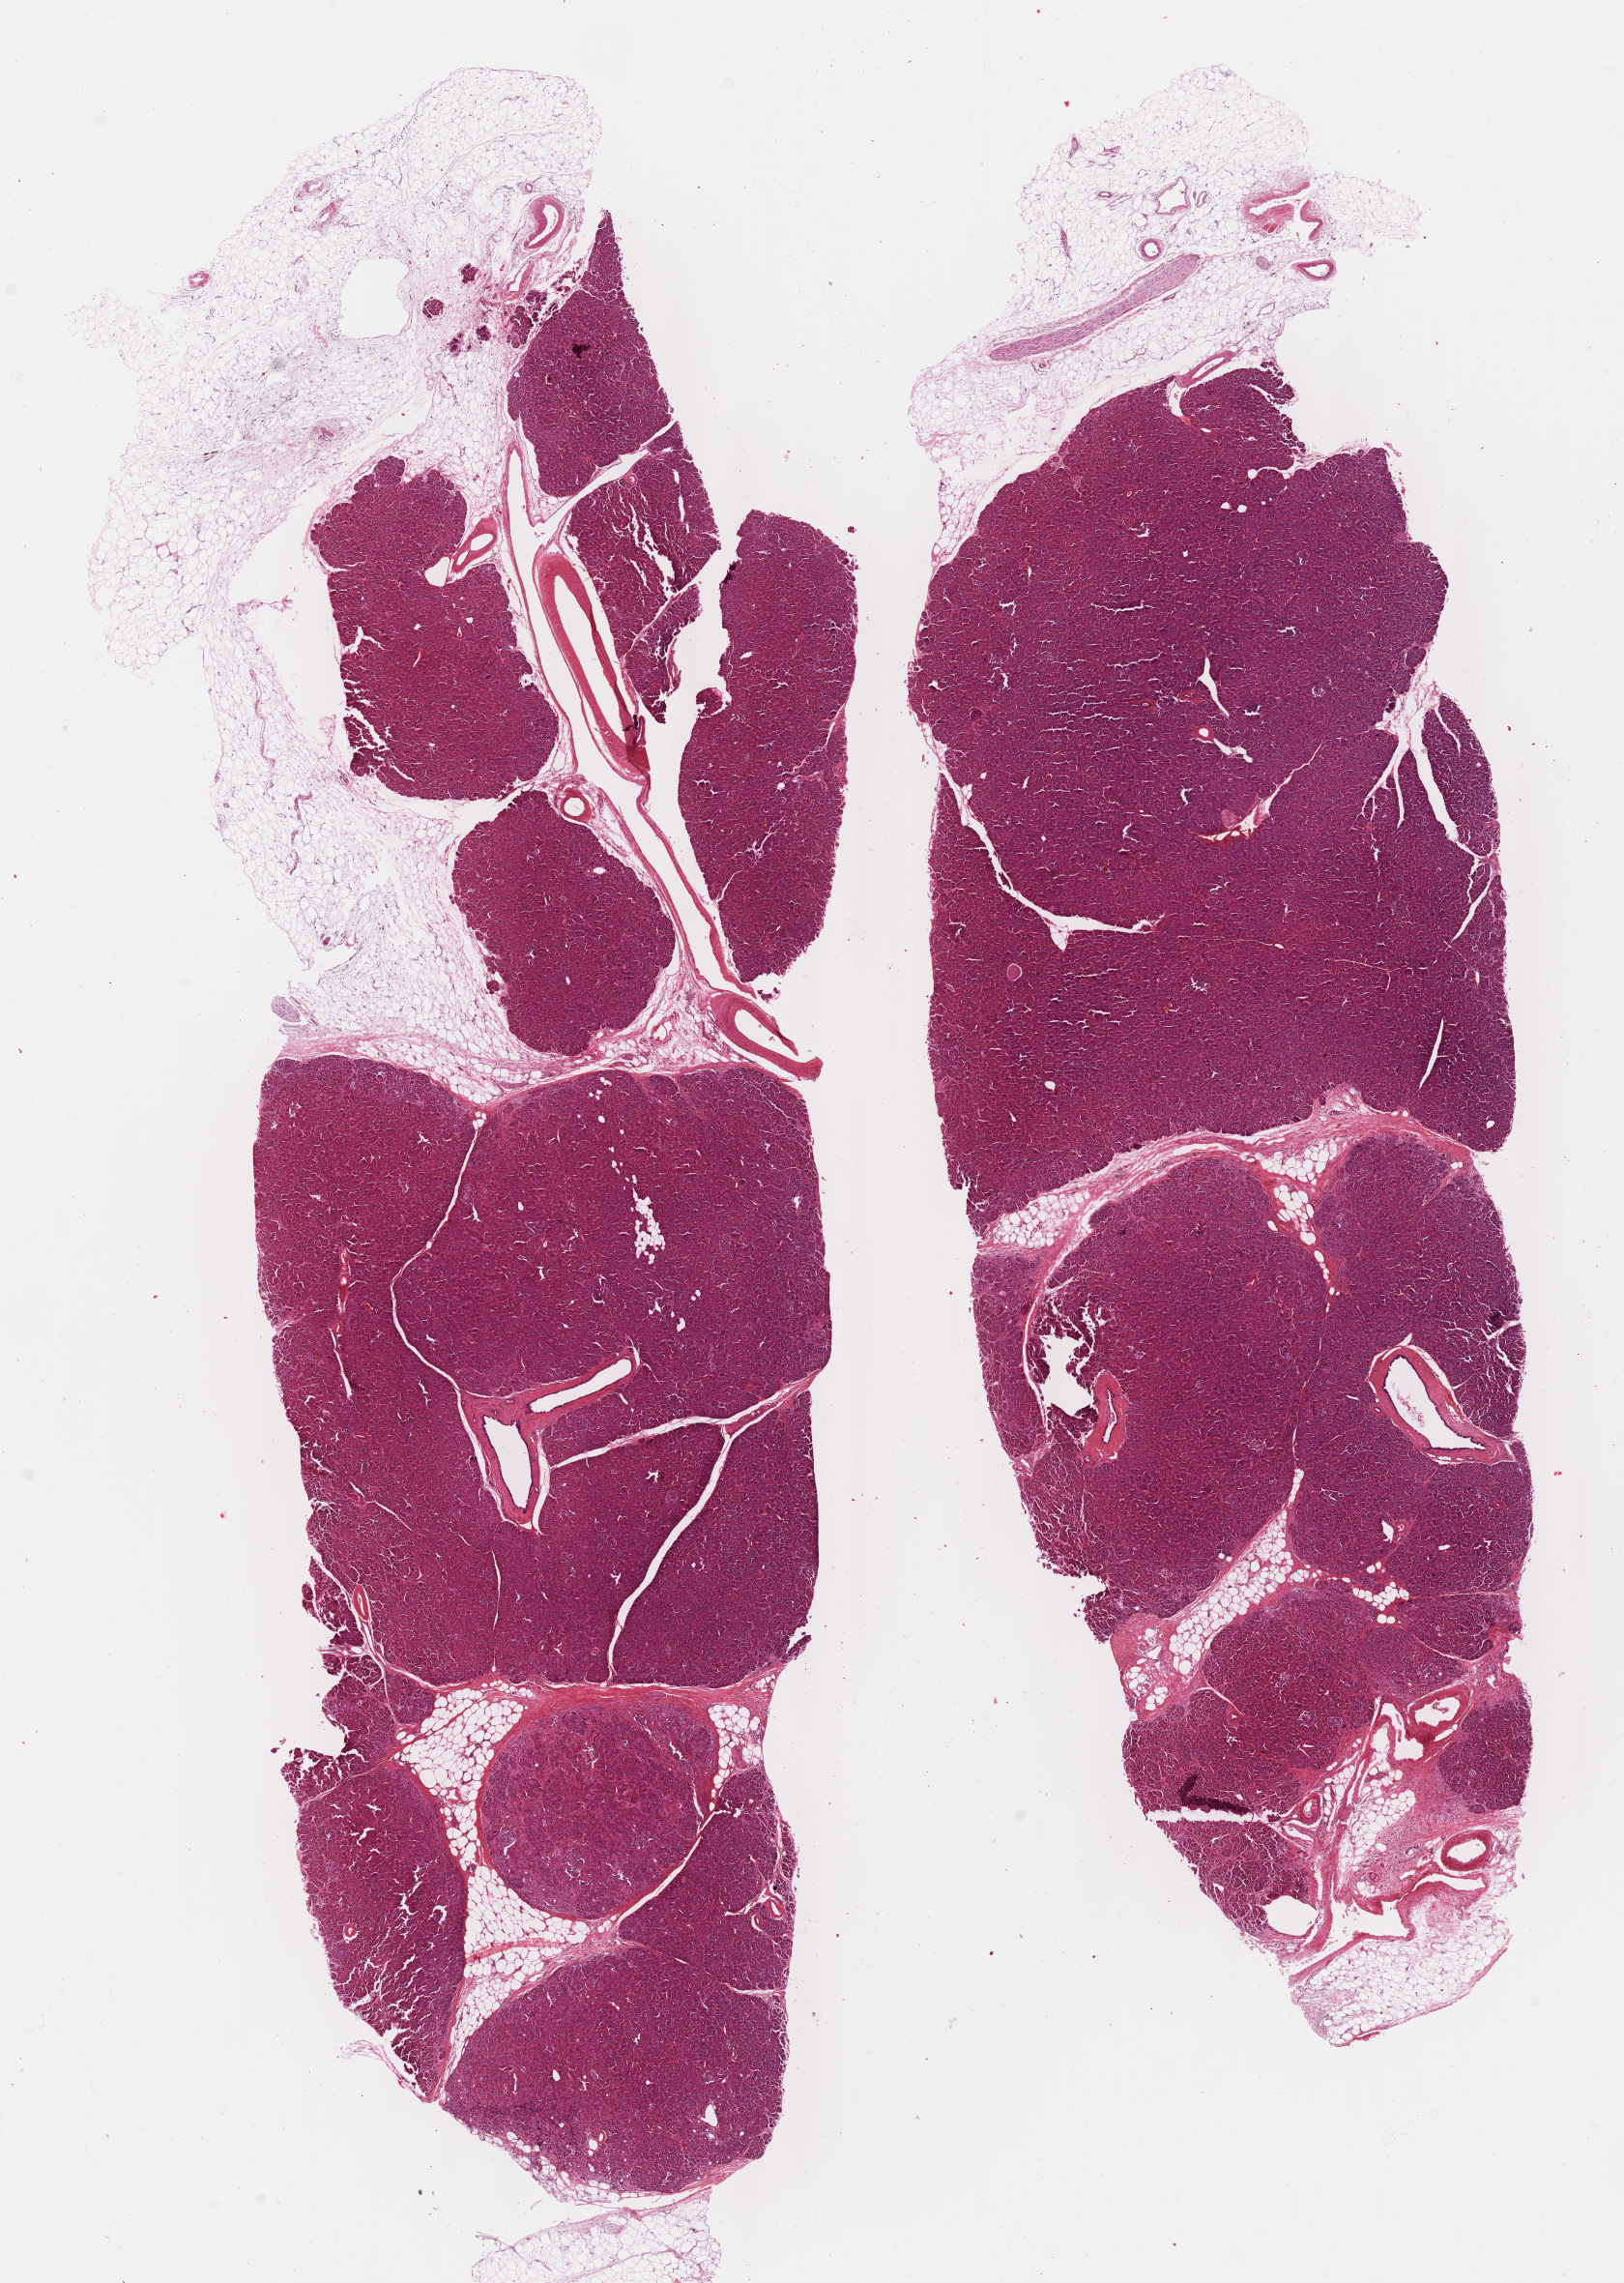
H&E whole-slide image, whole scanned area (about 13.6 x 19.1 mm, from a 40x scan) shown as a low-resolution overview; formalin-fixed paraffin-embedded (FFPE) diagnostic section; sample: solid tissue normal (non-tumour tissue), pancreas. Patient: male, age at initial diagnosis 70 years.
This section: solid tissue normal (non-tumour) sample from the same patient. Patient diagnosis: Infiltrating duct carcinoma, NOS.